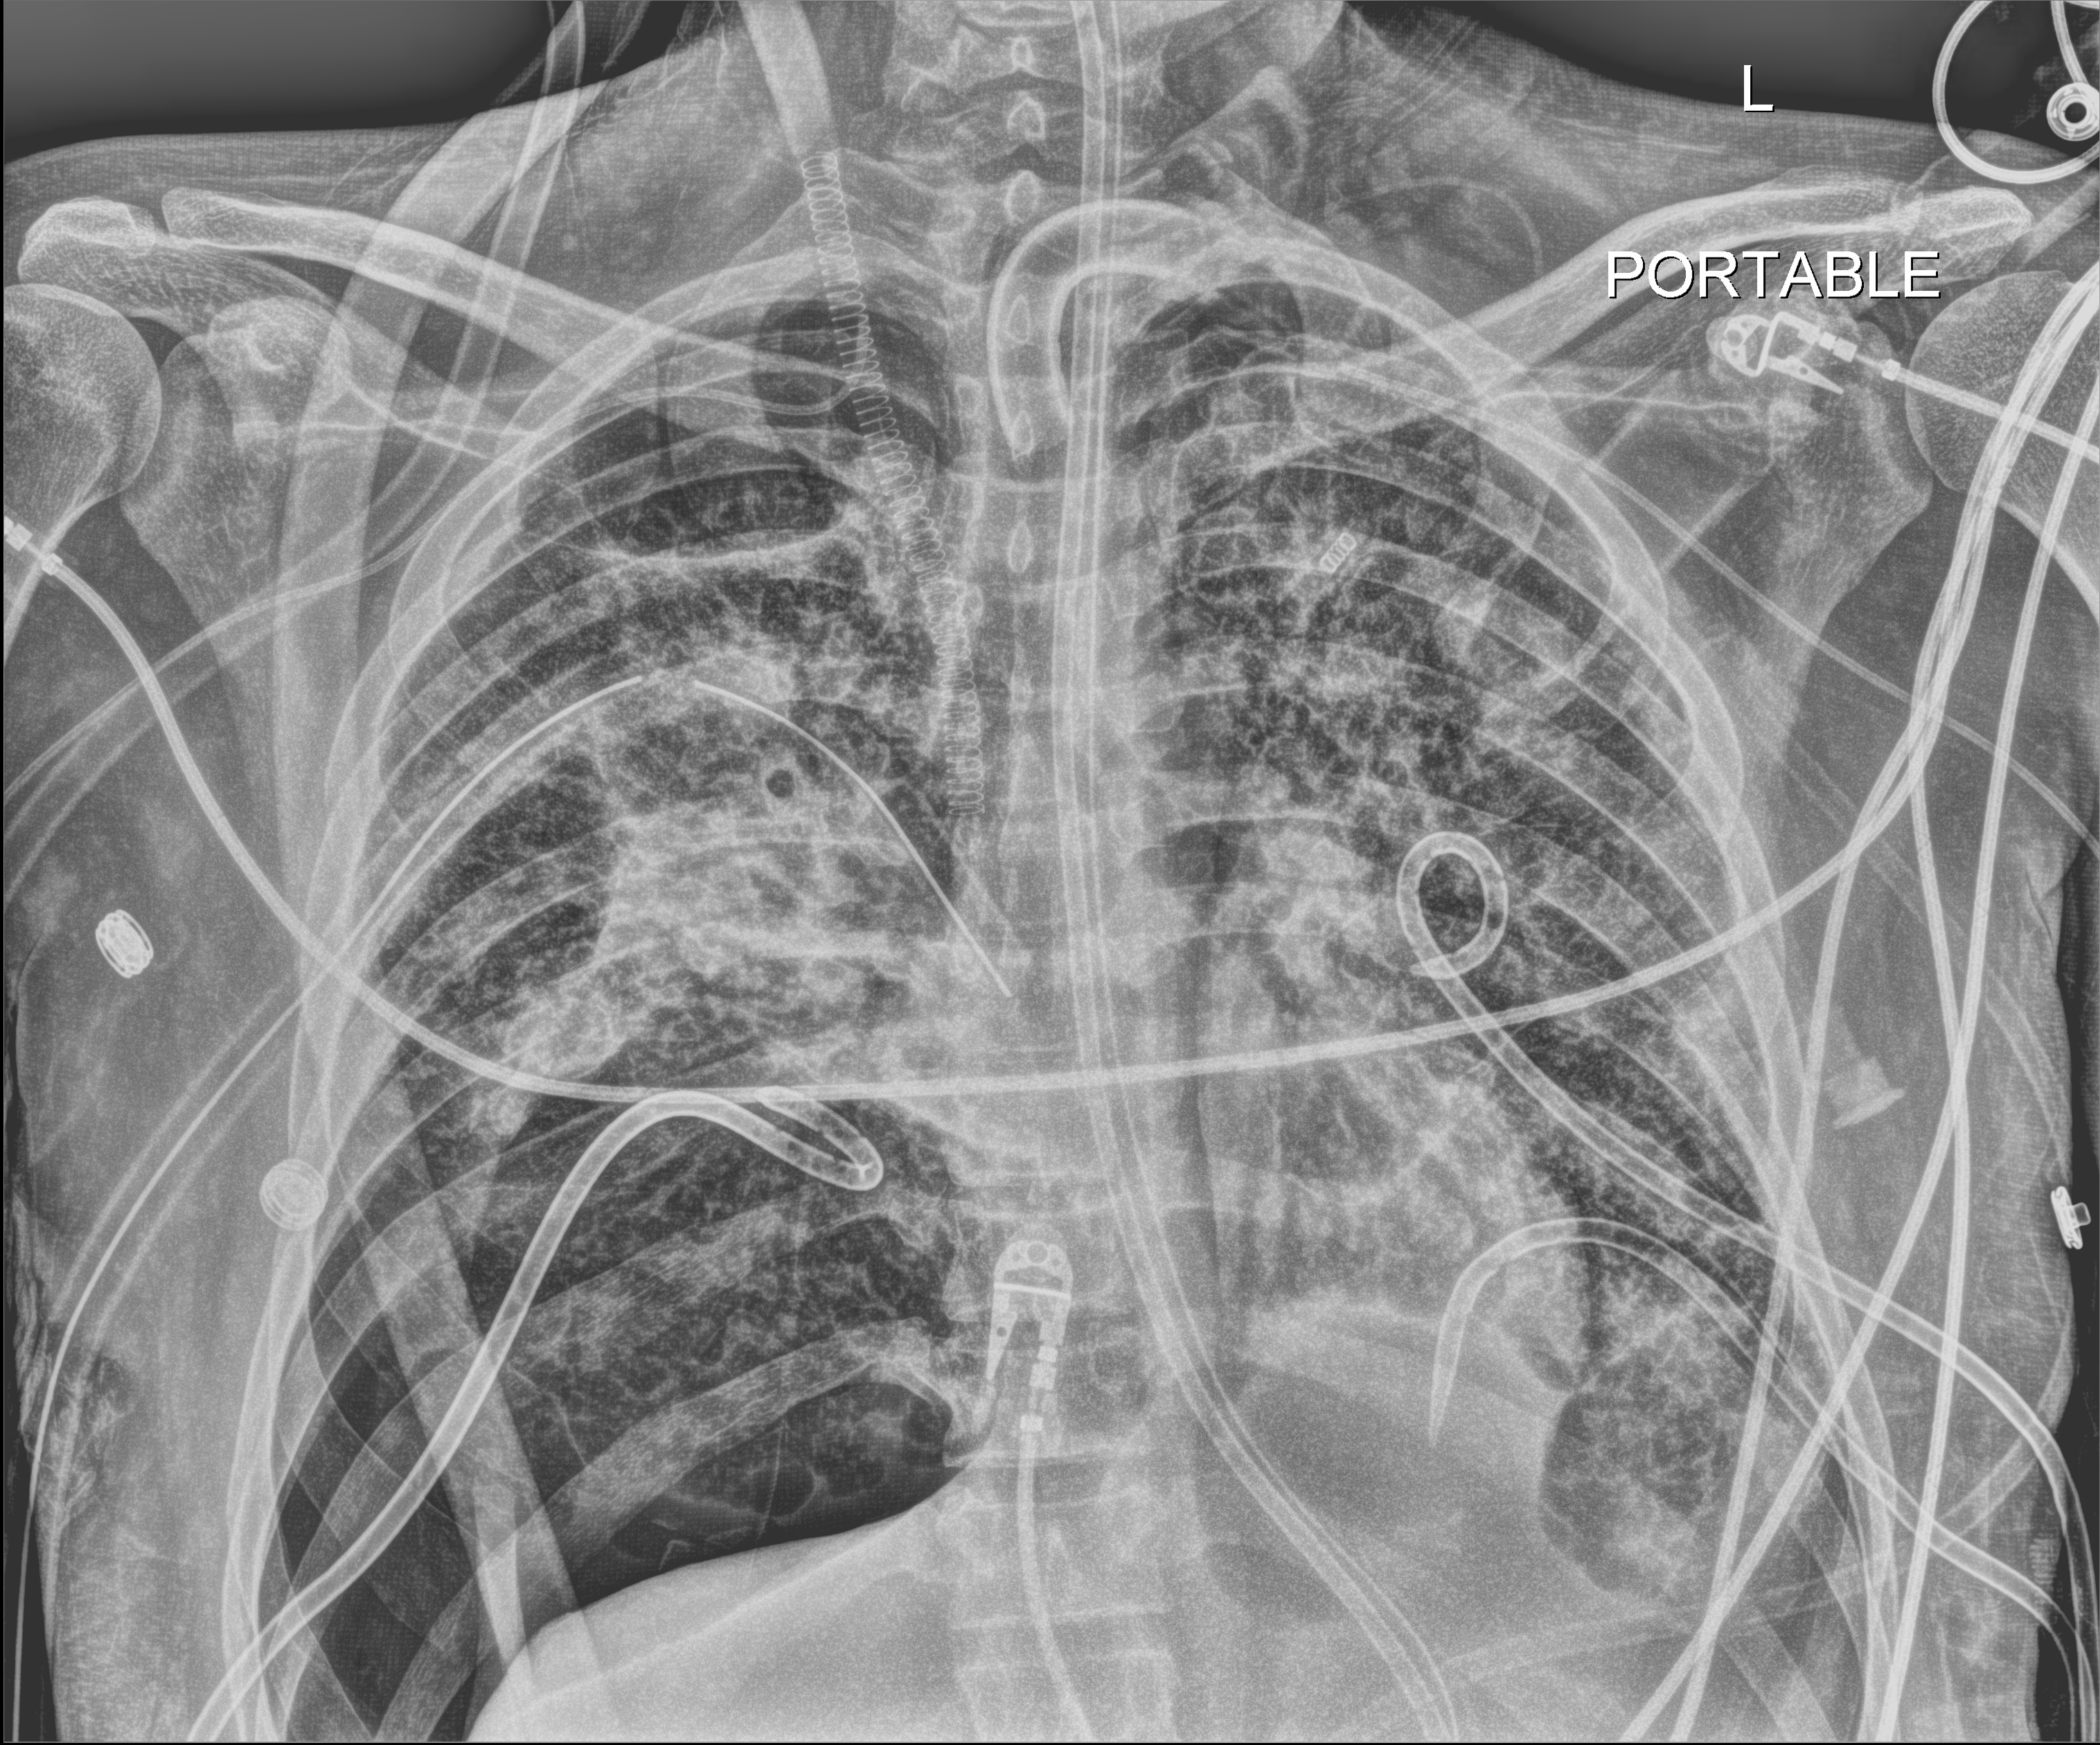
Portable chest radiograph, anteroposterior (AP) projection. Adult patient hospitalised with COVID-19, age 18–59 years.
From the hospital-stay record, not from the radiograph (when in the stay this image was taken is not recorded):
- chronic kidney disease (admission record): no
- admitted to intensive care during this hospital stay: yes
- mechanically ventilated during this hospital stay: yes